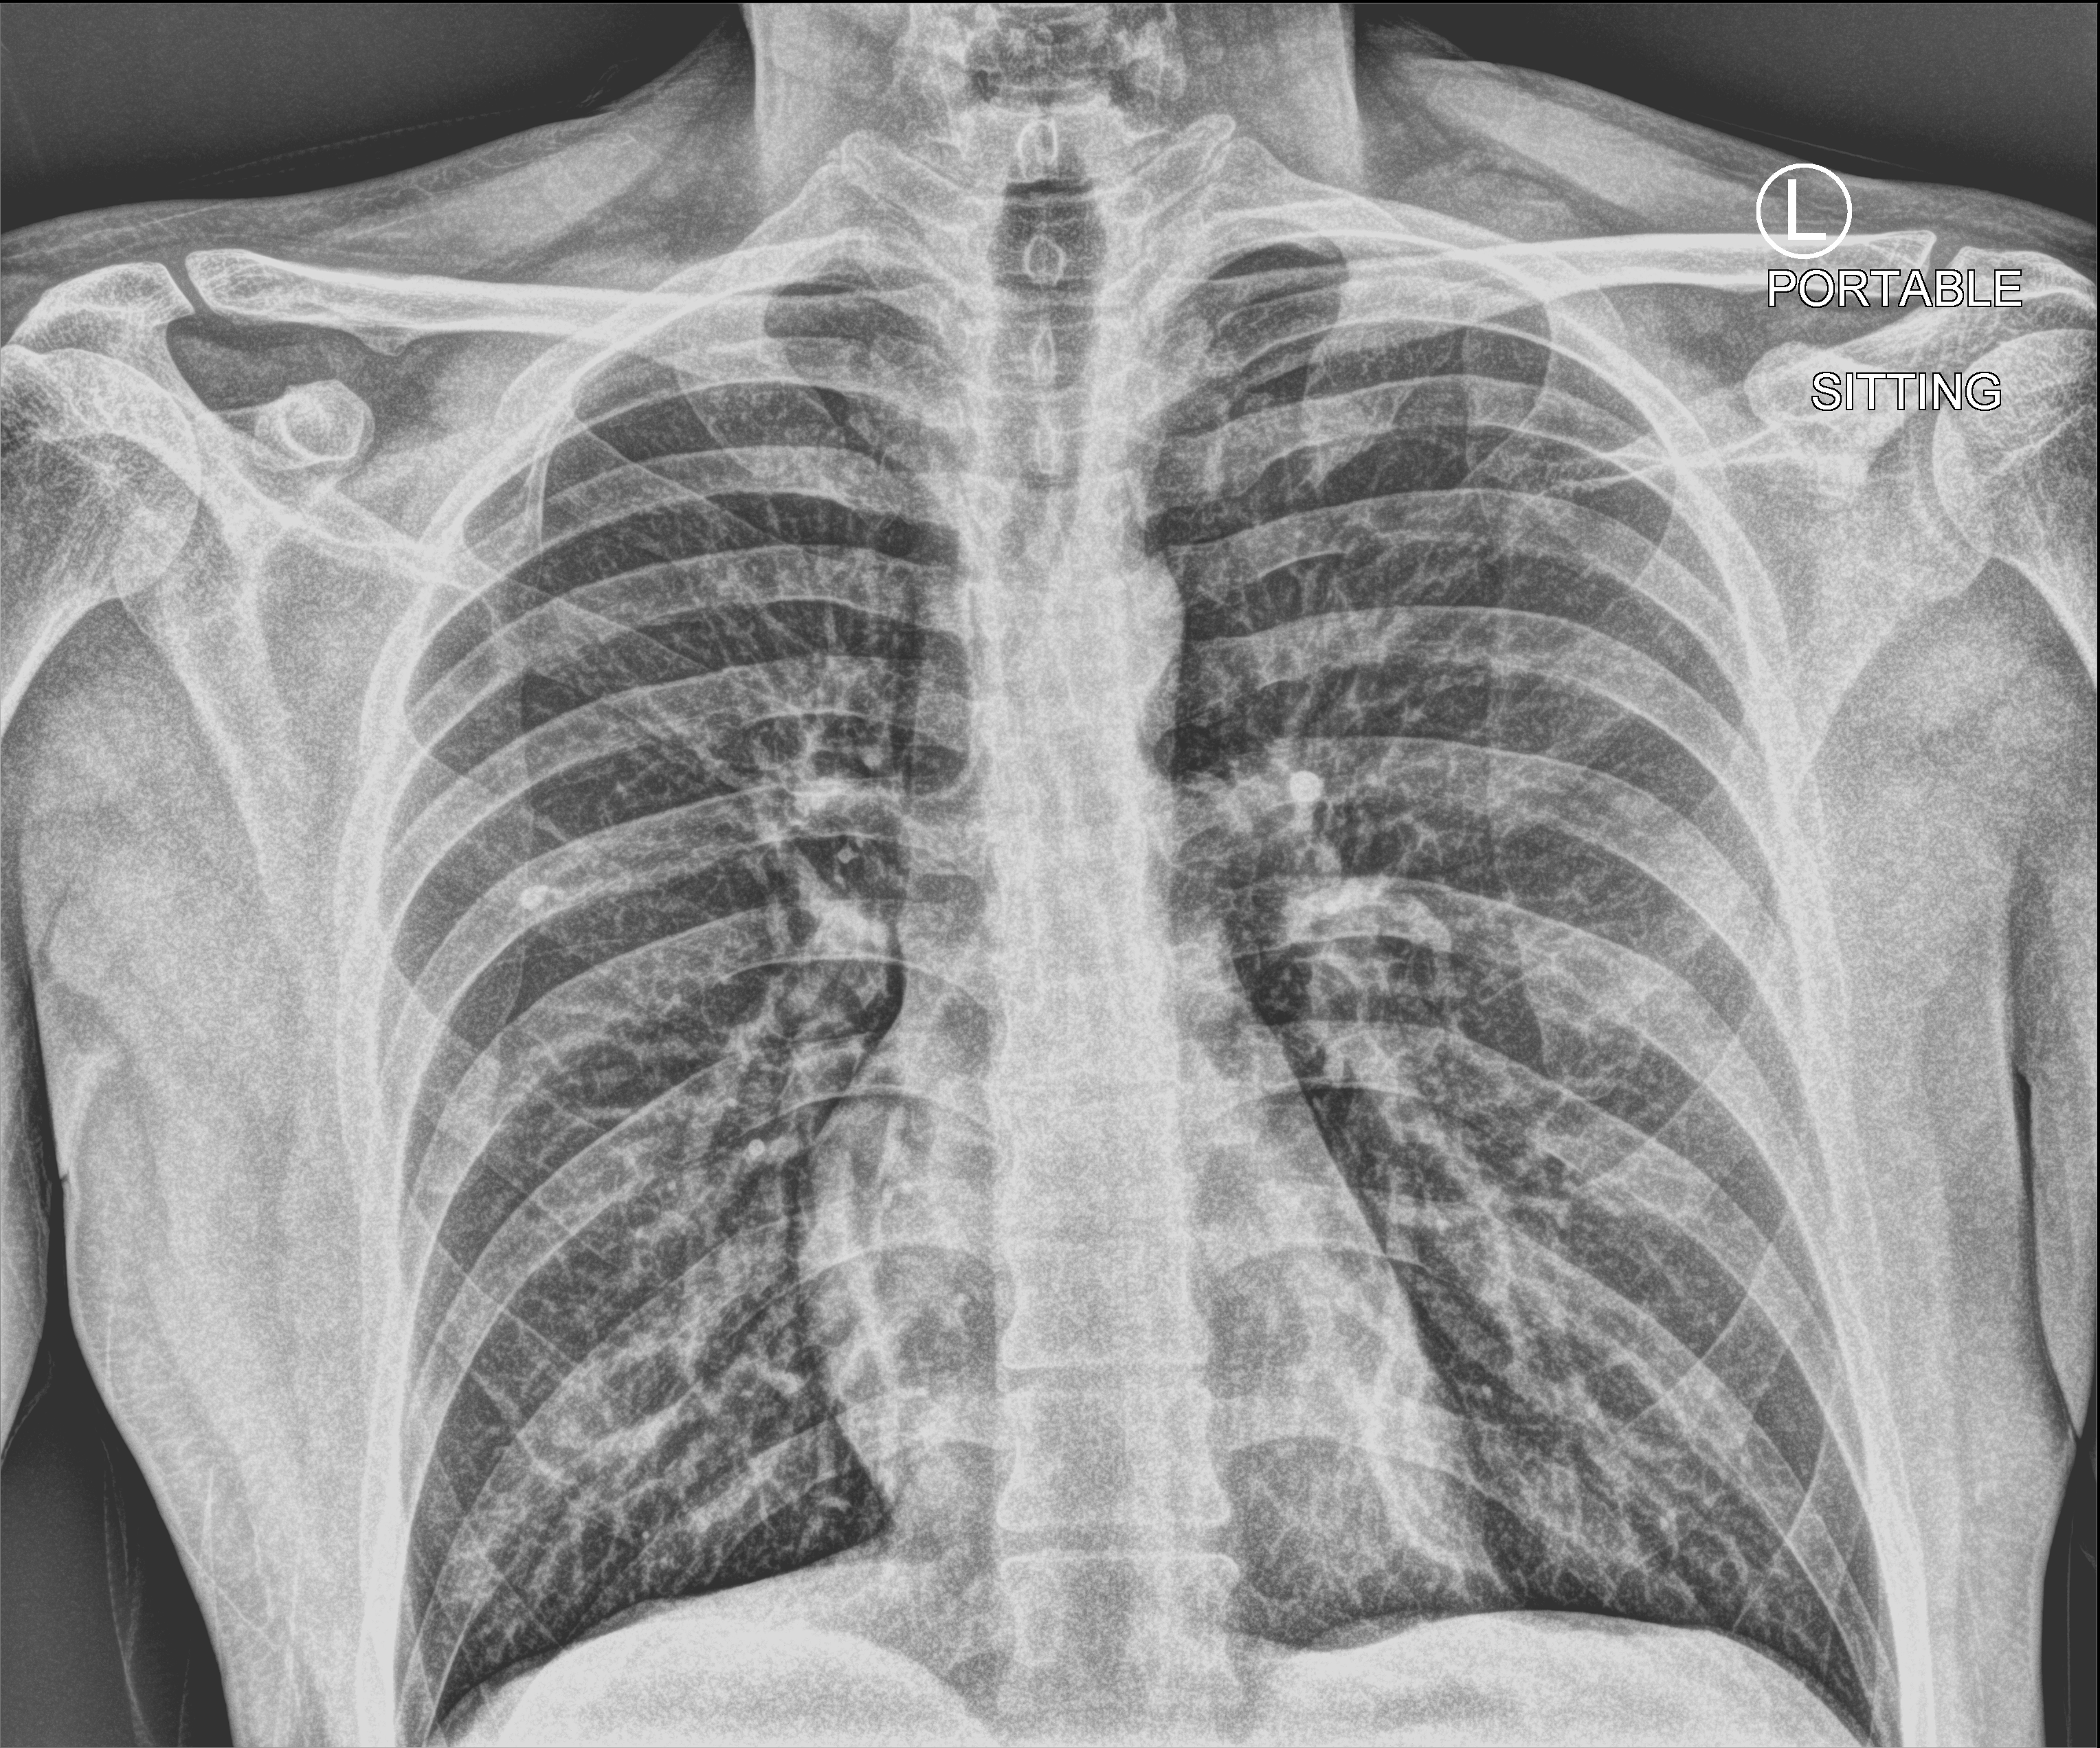
Bedside chest radiograph (computed radiography), anteroposterior (AP) projection. Patient hospitalised with COVID-19; male, aged 18–59 years.
From the hospital-stay record, not from the radiograph (when in the stay this image was taken is not recorded):
- diabetes (admission record): no